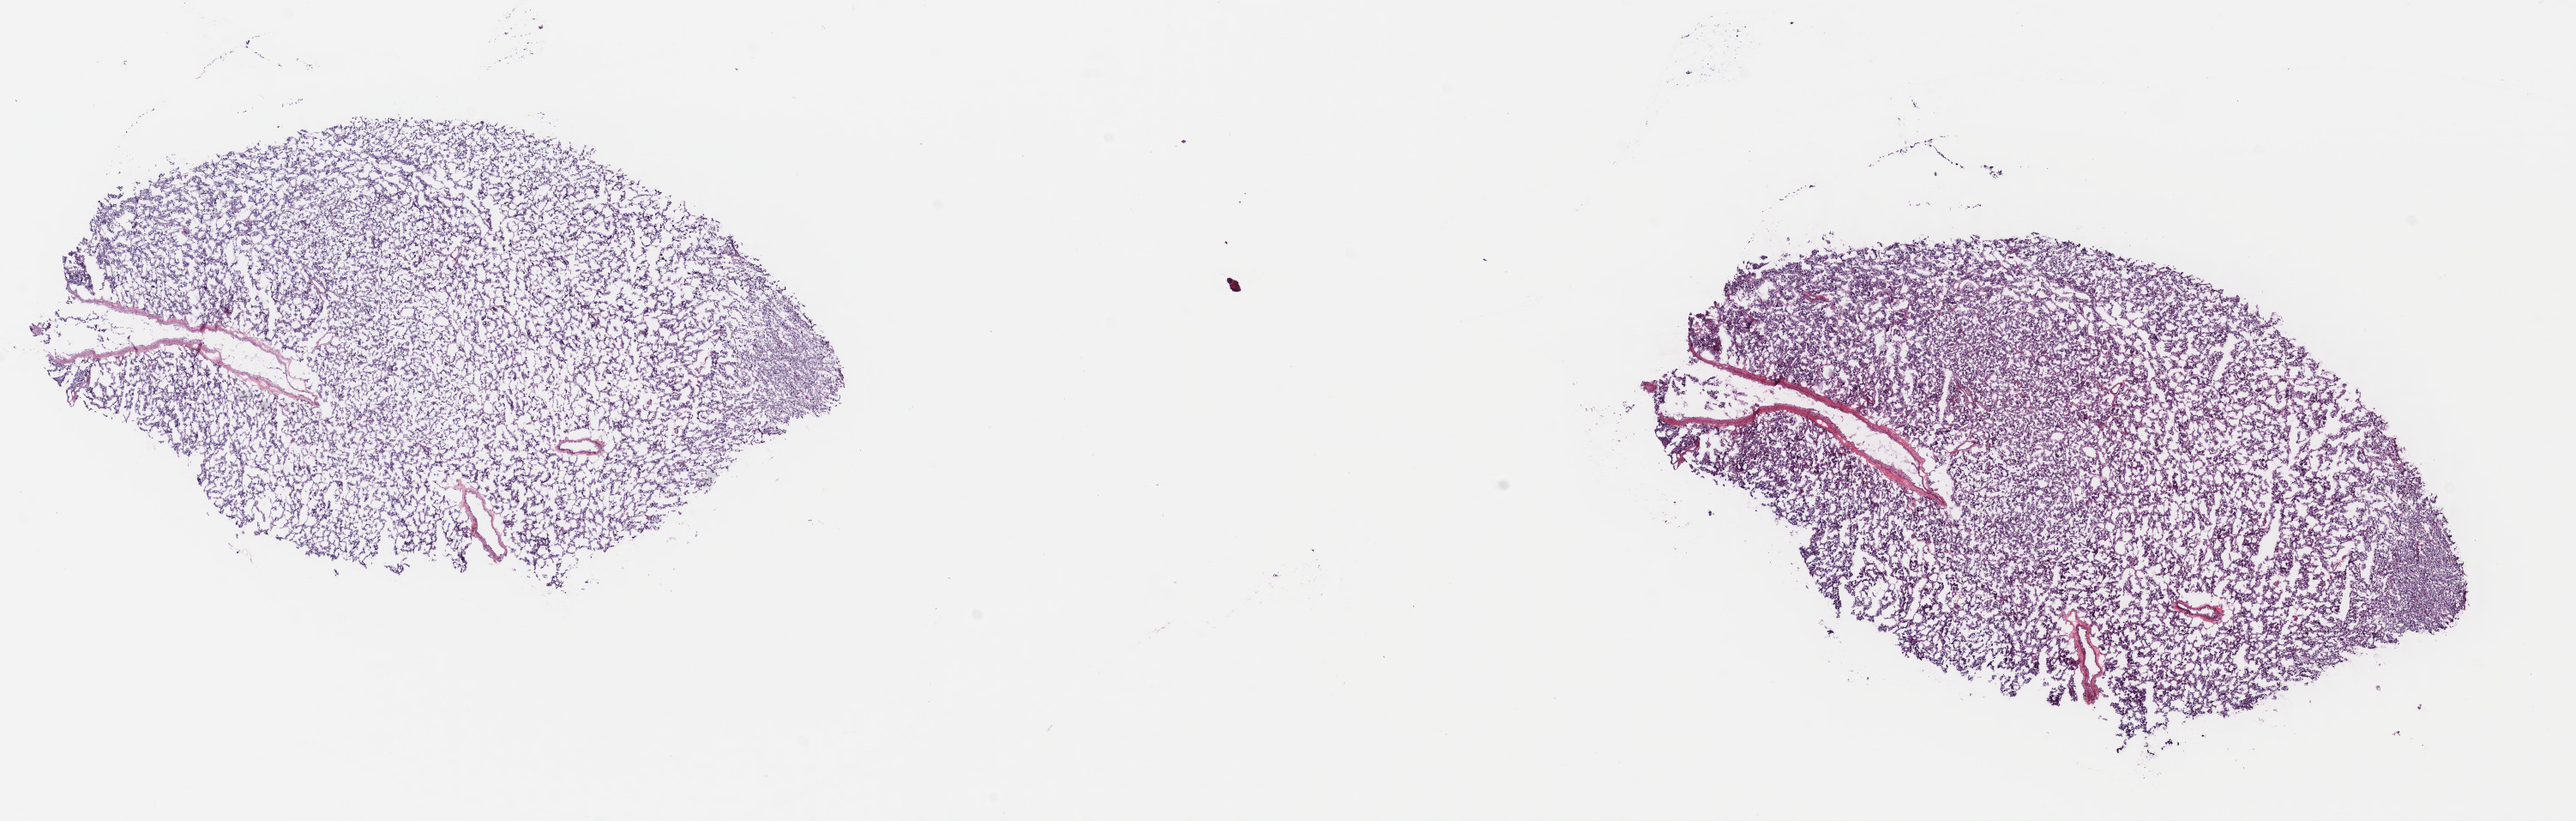
Whole-slide histology image, H&E-stained, whole scanned area (about 23.6 x 7.5 mm, from a 40x scan) shown as a low-resolution overview, frozen section, primary tumour sample from the adrenal gland. Patient: male, age at initial diagnosis 48 years. Composition of this section per pathologist review: tumour cells 100%, tumour nuclei 93%.
Histologic diagnosis: Pheochromocytoma, NOS (cortex of adrenal gland).